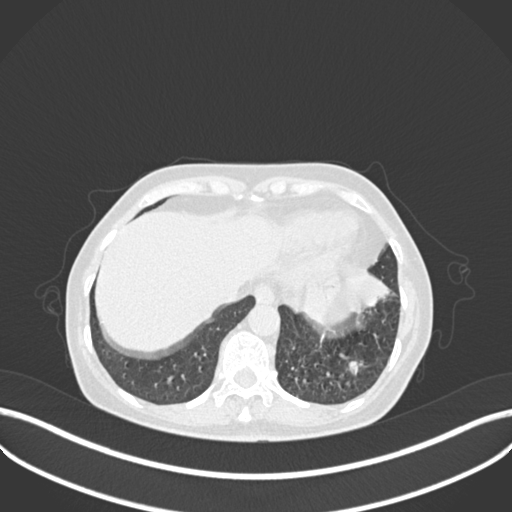
Chest CT, one axial slice; slice 49 of 270 in the series (ordered by position); 120 kVp; lung window (W 1500 / L -600 HU); 512 × 512 image matrix, field of view 400 × 400 mm. Patient: female, 63 years. Case-level facts recorded for this patient, not image findings: clinical TNM (as recorded): T1b N0 M0.
Outlined on this slice (bounding box drawn by a radiologist):
- lung tumour (recorded histology: adenocarcinoma): bounding box (x1, y1, x2, y2) in pixels: (343, 256, 391, 311)